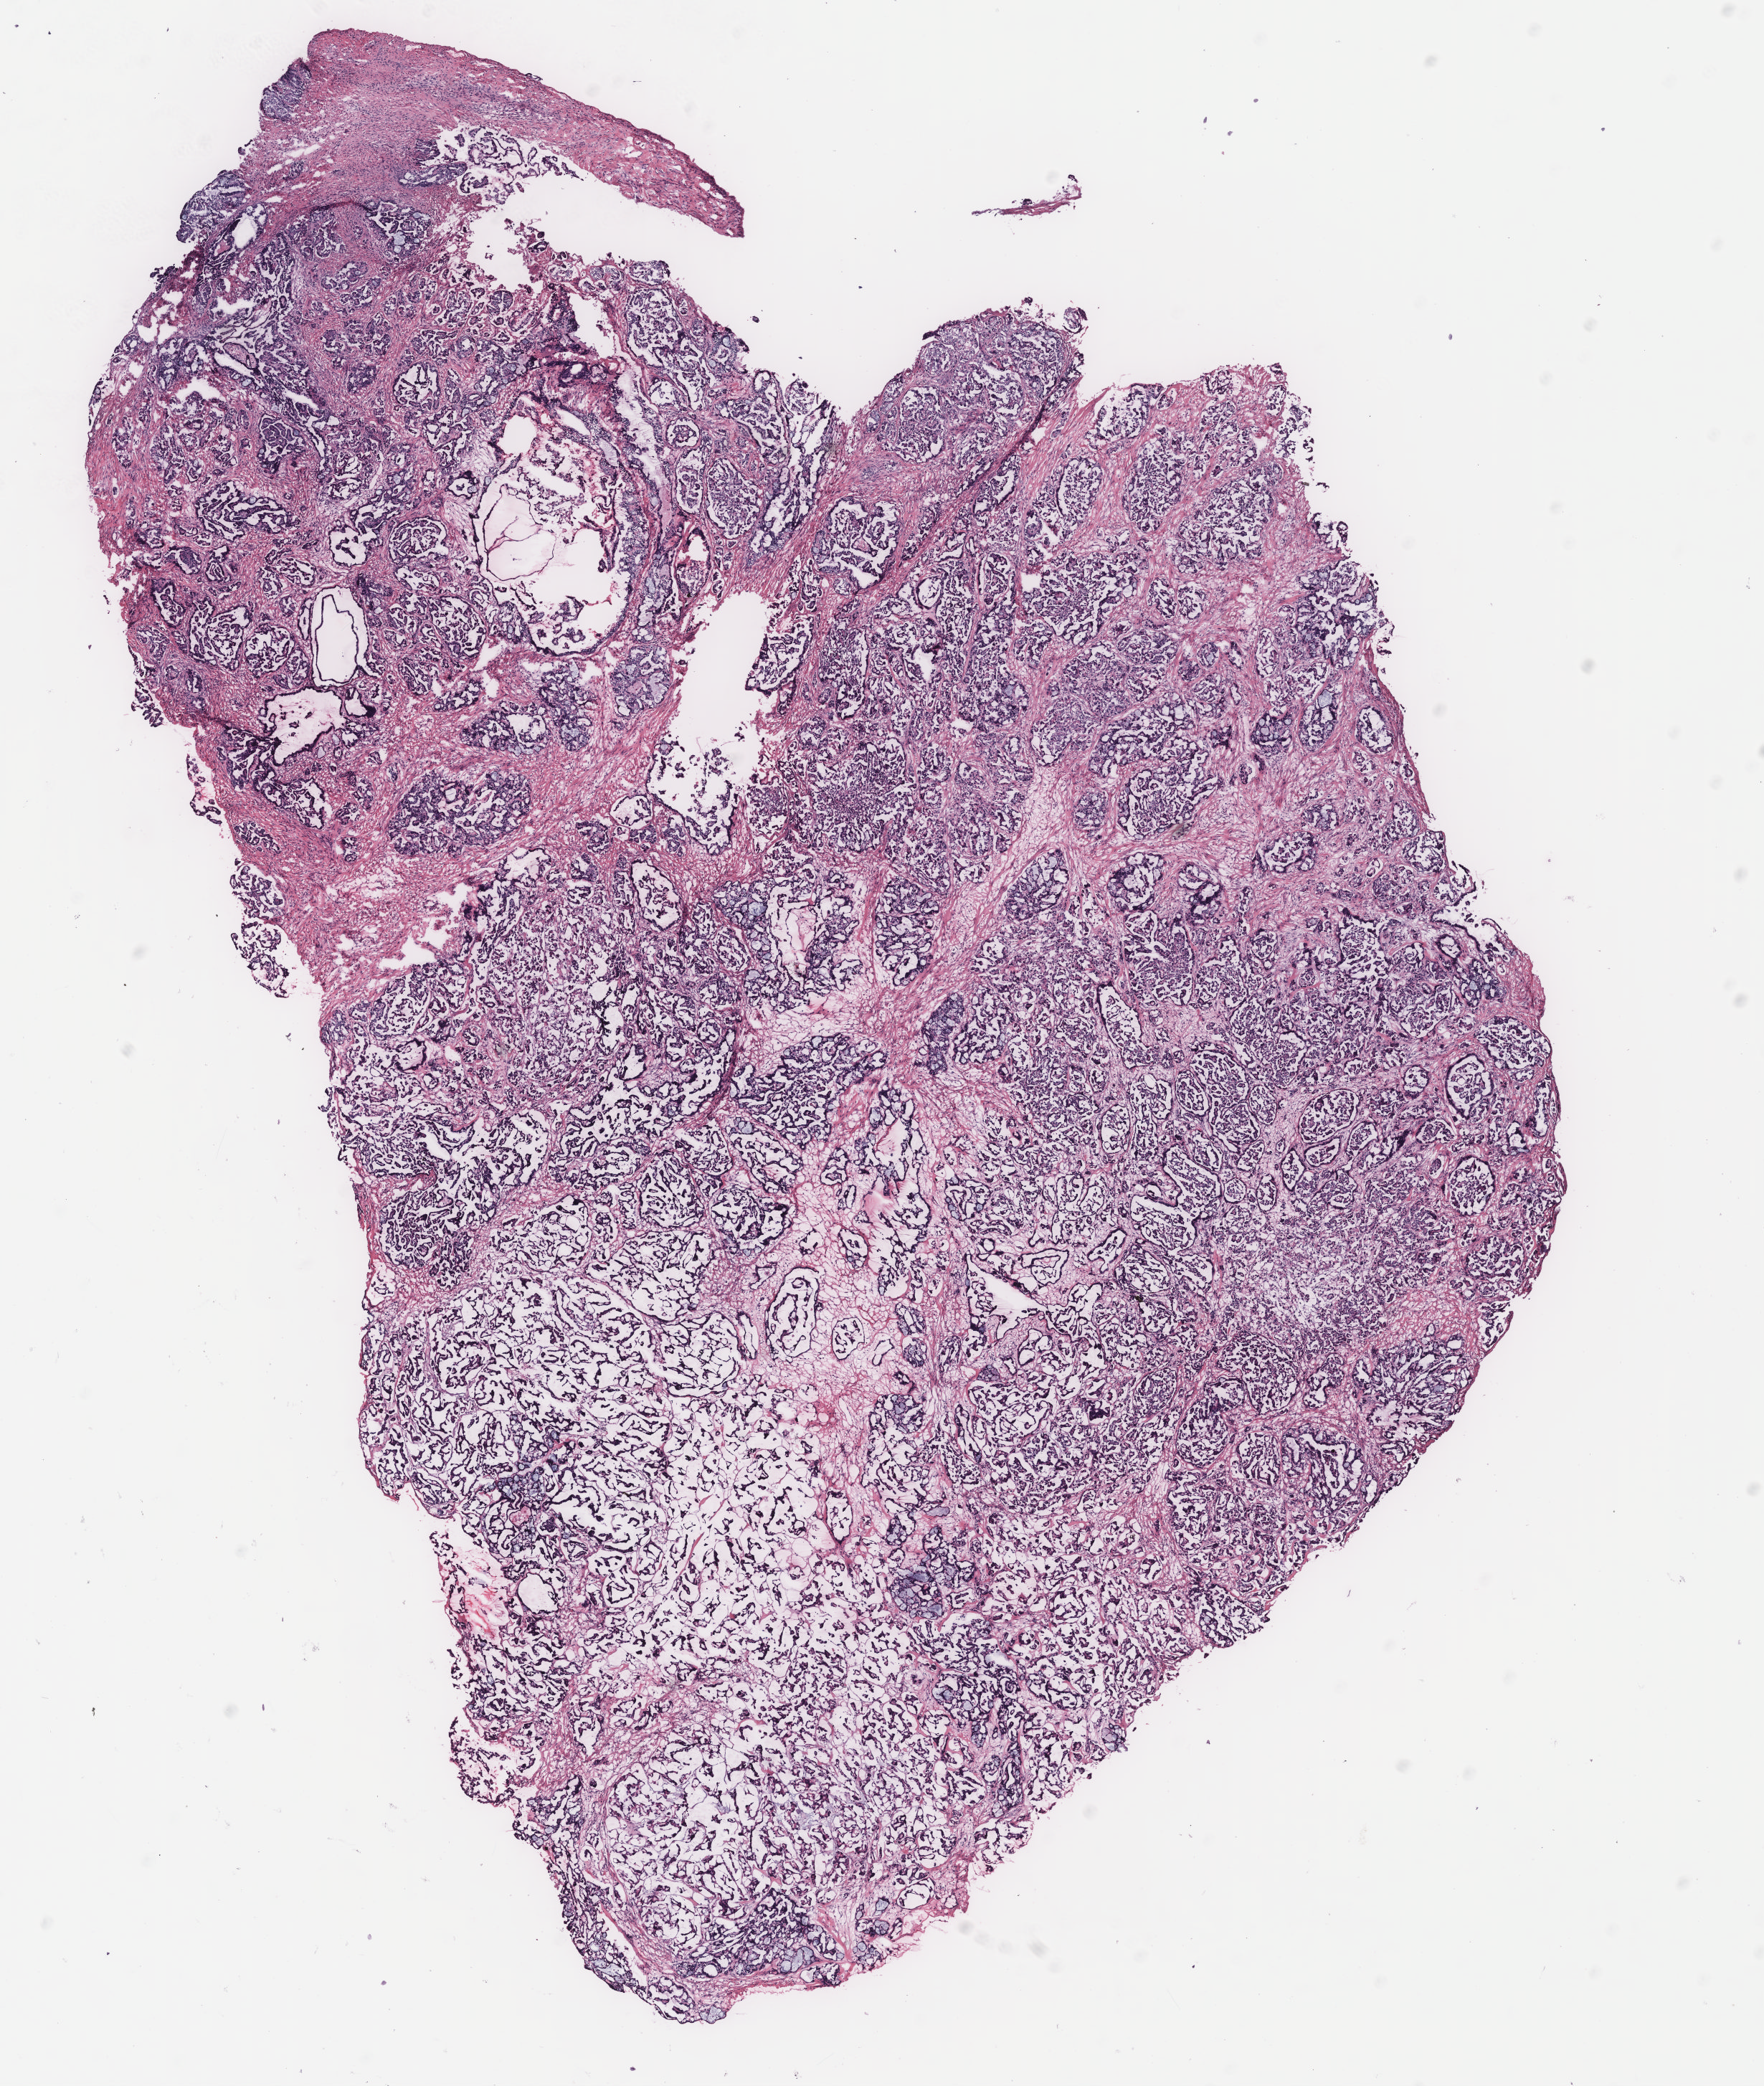
H&E-stained whole-slide image — a low-resolution overview of the entire scanned area, about 9.8 x 11.6 mm (slide scanned at 40x). Tumour tissue sample, ovary. Female, 73 y/o.
Histologic diagnosis: Serous adenocarcinoma, NOS.